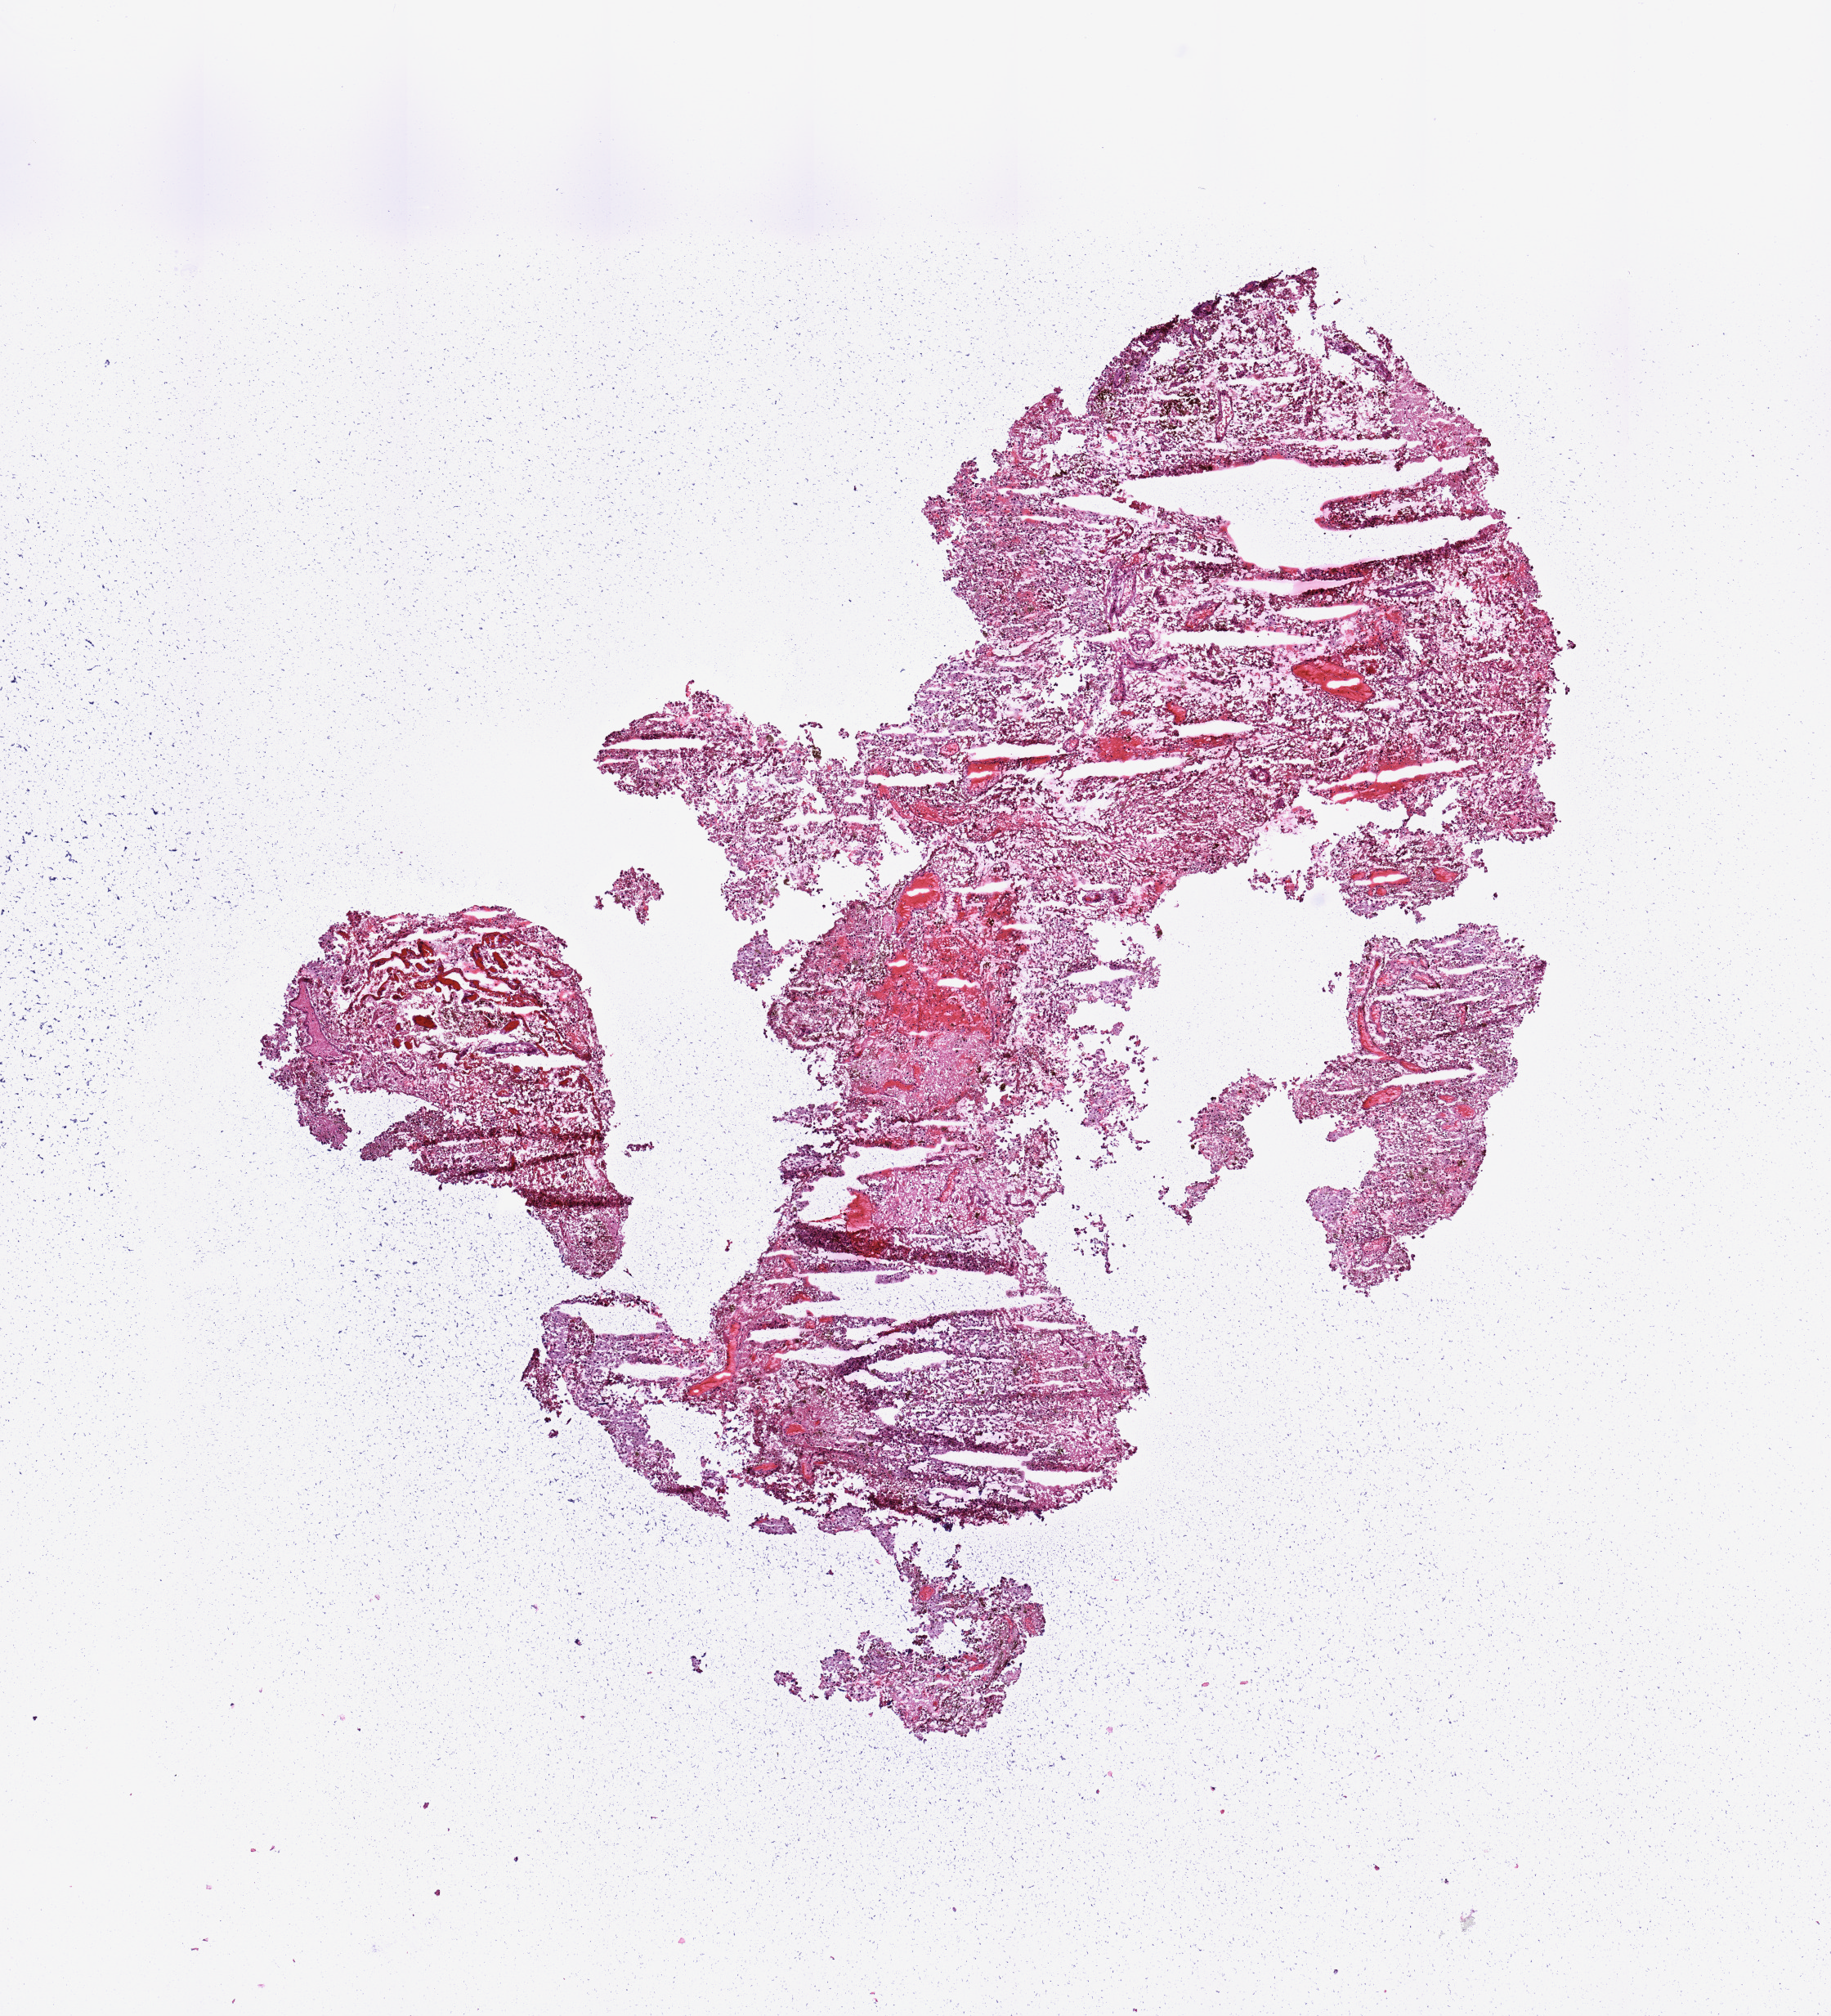
Digitized H&E tissue section (whole slide), shown as a low-resolution overview of the whole scanned area (about 8.9 x 9.8 mm, slide scanned at 20x); melanoma tumour tissue; sampled site not recorded. Patient: male, age 75 years.
• primary tumour site (as recorded): head & neck
• patient diagnosis (cohort enrolment): cutaneous melanoma (skin)